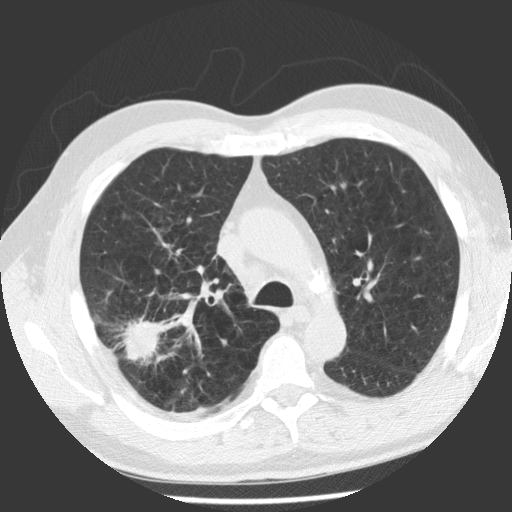
Low-dose screening chest CT, axial slice, baseline screening round, lung window (W 1500 / L -600 HU), 2.5 mm slice thickness, standard (soft-tissue) reconstruction kernel (STANDARD), 140 kVp, slice 77 of 112 in the series, 512 × 512 image matrix. Male, age 62 years at enrolment.
Expert reader's lesion annotation, bounding box (x1, y1, x2, y2) in pixels: (108, 300, 183, 372). The screening reader recorded 2 non-calcified nodules or masses ≥4 mm on this exam (right upper lobe, right upper lobe); which of them this box marks is not recorded. Official screen result: positive, change unspecified: nodule(s) >= 4 mm or enlarging nodule(s), mass(es), or other non-specific abnormalities suspicious for lung cancer. Later outcome: lung cancer diagnosed 71 days after this screen — adenocarcinoma, NOS, right upper lobe, poorly differentiated (G3), stage IV (AJCC 6th edition), 30 mm at pathology.